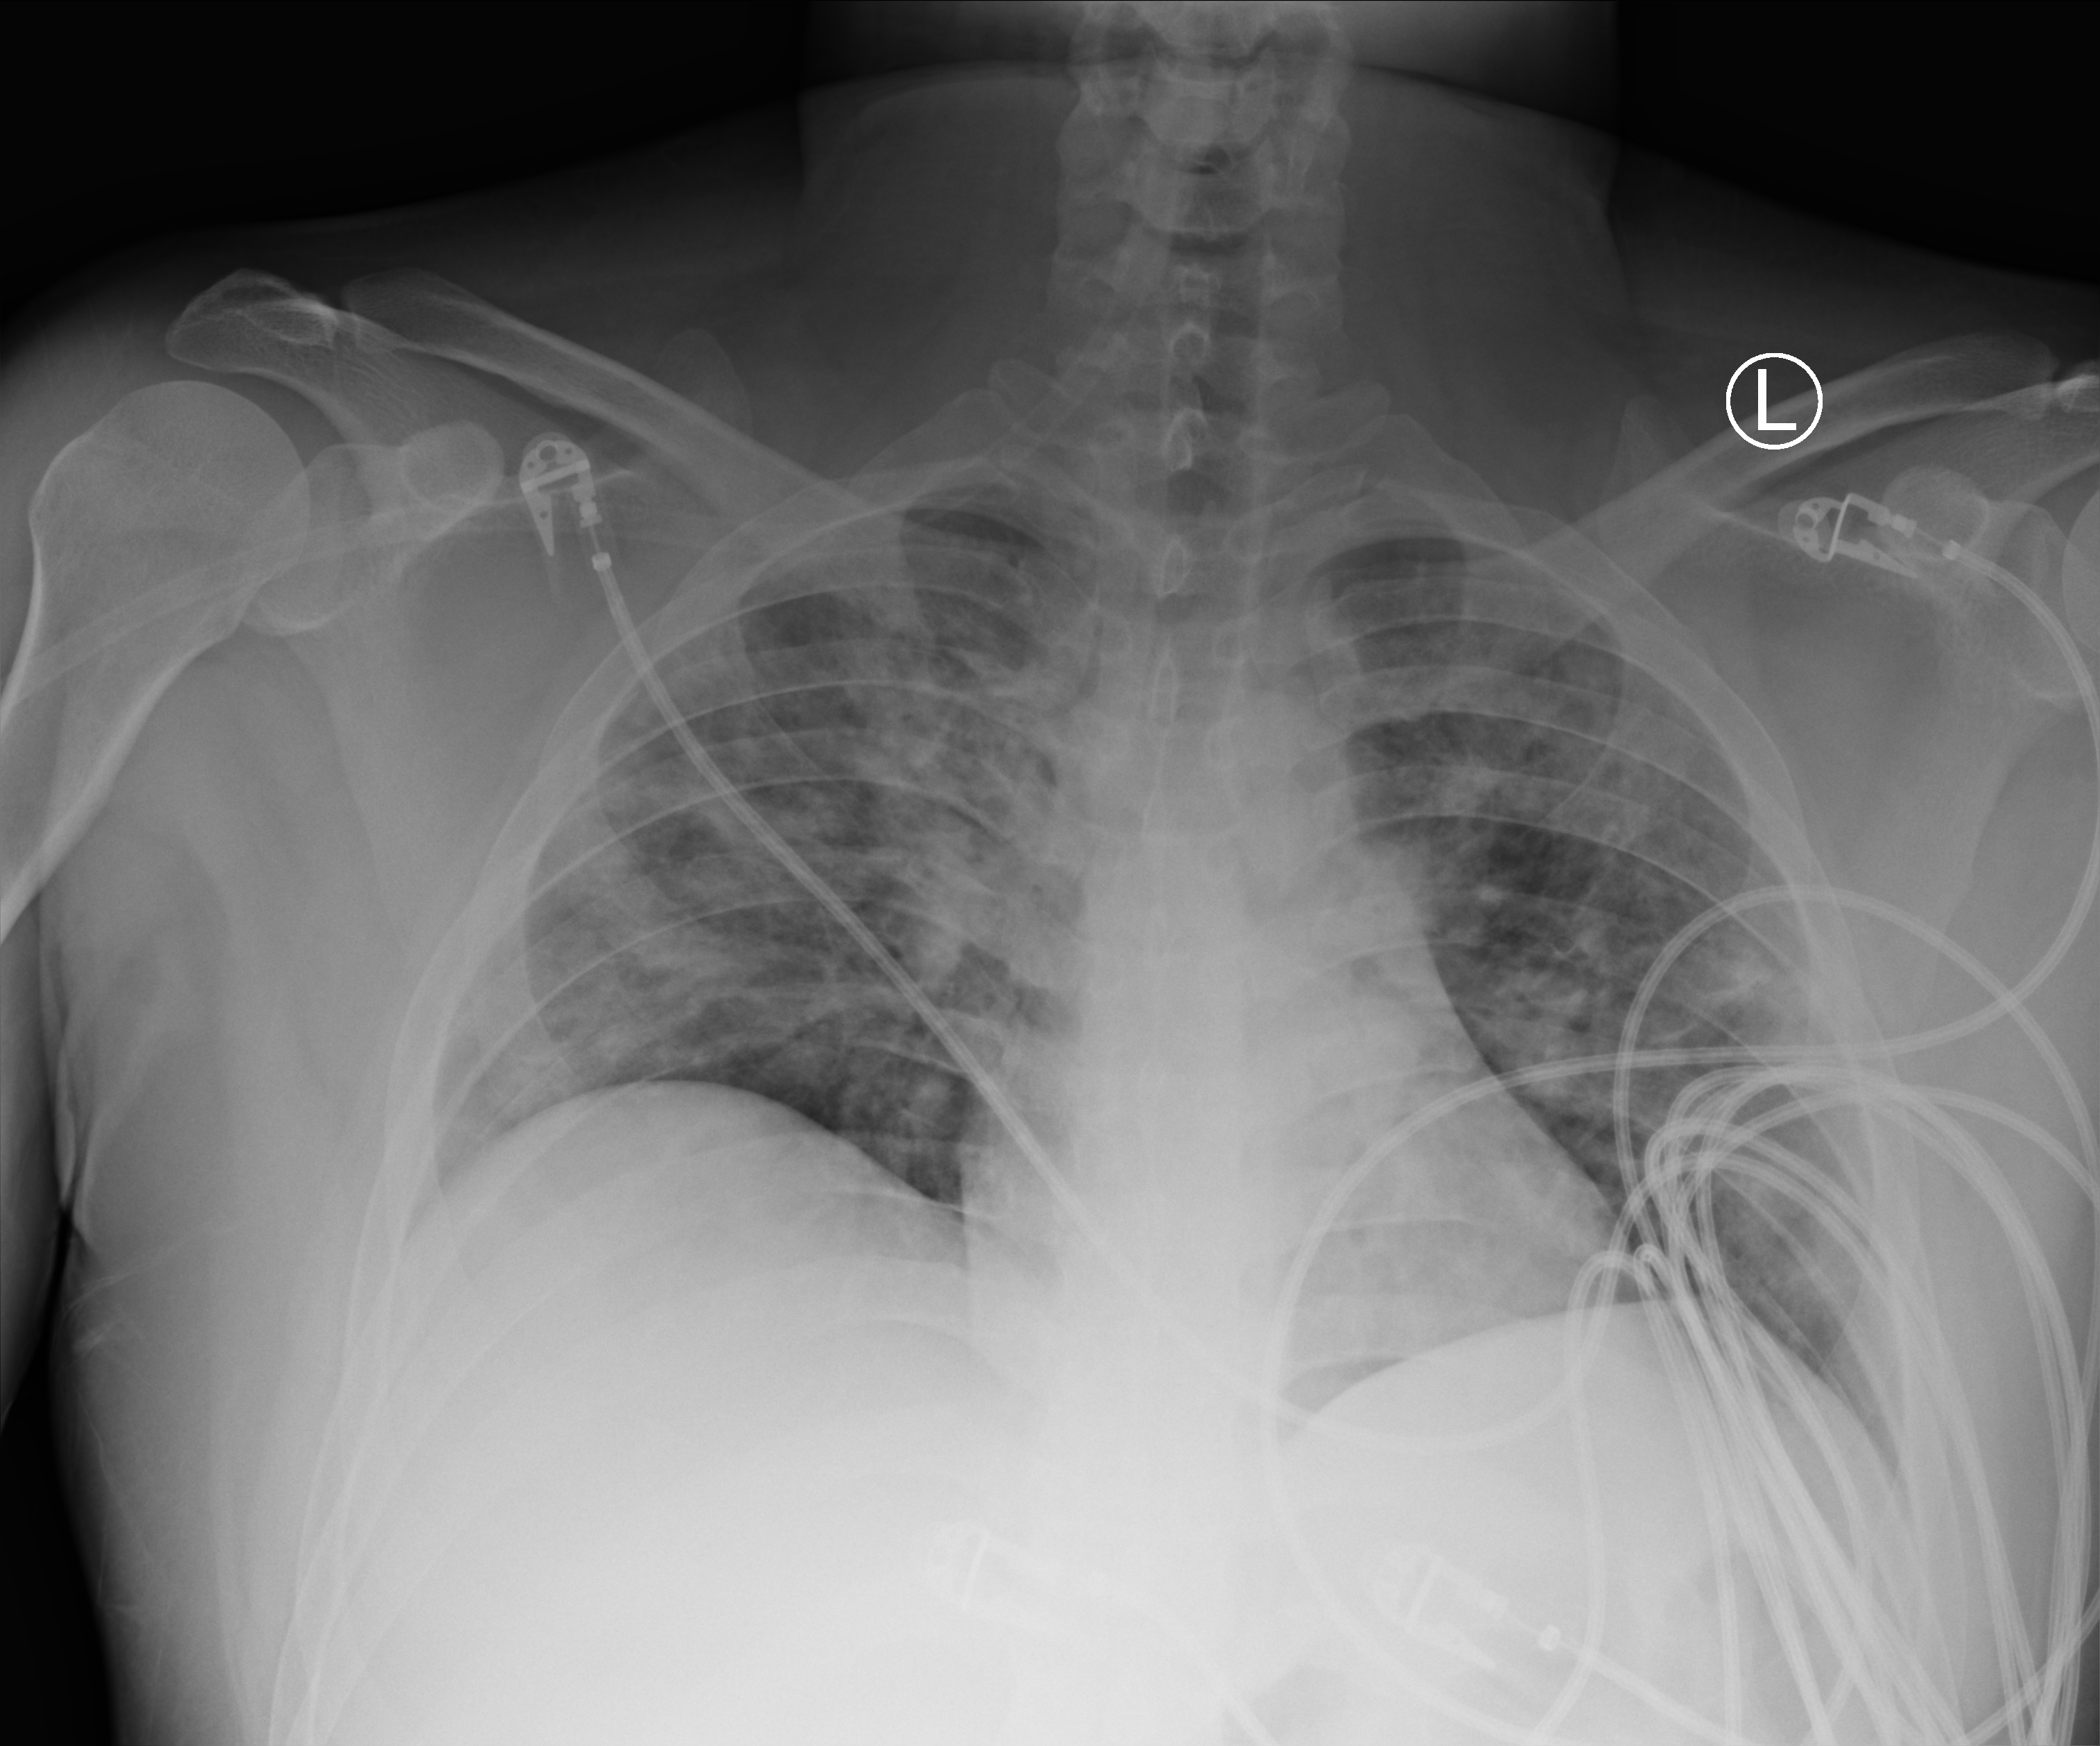
Portable chest radiograph, anteroposterior (AP) projection. Patient hospitalised with COVID-19; male, aged 18–59 years.
Hospital-stay facts (about this admission, not read from this image; timing relative to this image not recorded):
- admitted to intensive care during this hospital stay: yes
- mechanically ventilated during this hospital stay: yes
- other chronic lung disease (admission record): no